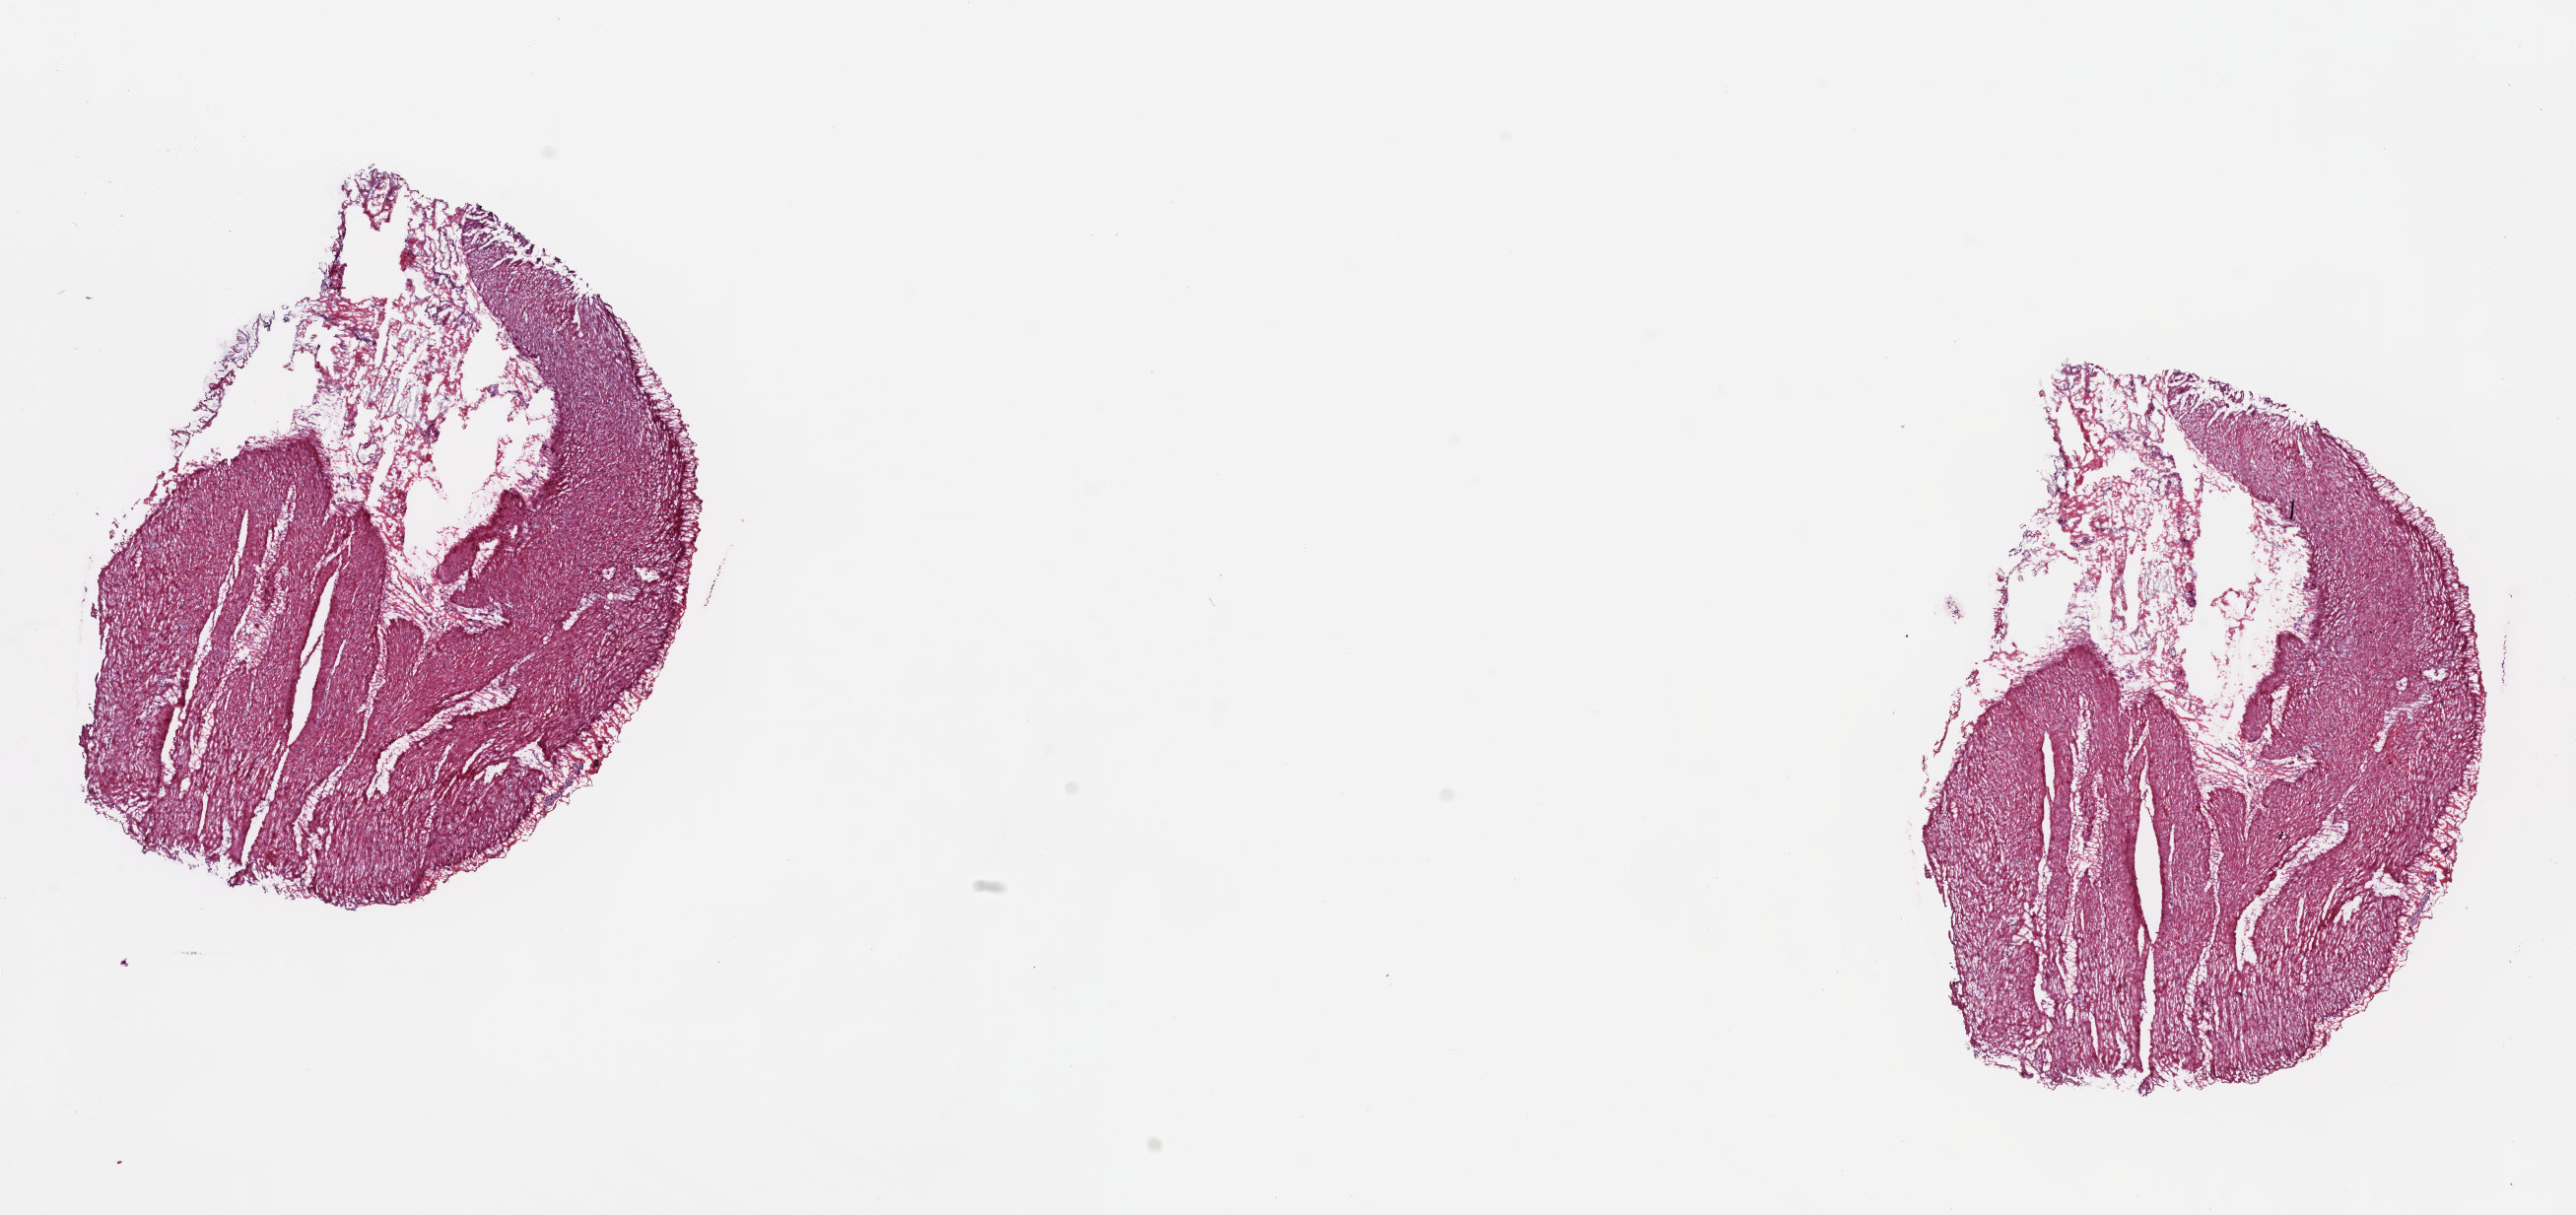
Digitized Hematoxylin and eosin (H&E) stained tissue section (whole slide) — a low-resolution overview of the entire scanned area, about 20.6 x 9.7 mm (acquisition: 20x scan). Frozen section. Sample: solid tissue normal (non-tumour tissue), stomach. Male, age 54 years at initial diagnosis. Pathologist review of this section (percent, as recorded): tumour cells 0%, tumour nuclei 0%, normal cells 100%, stromal cells 0%, necrosis 0%. Infiltration values recorded for this section: lymphocyte infiltration 0%, monocyte infiltration 0%, neutrophil infiltration 0%.
This section: solid tissue normal (non-tumour) sample from the same patient. Patient diagnosis: Tubular adenocarcinoma (gastric antrum).